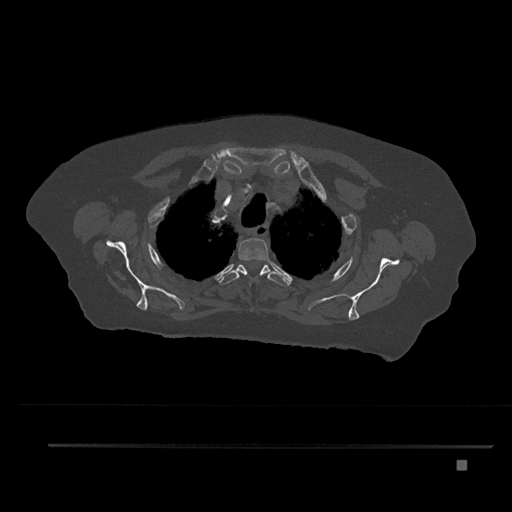
CT including the spine, one axial slice; slice 650 of 797 in the series (ordered by position); reconstruction kernel Br40s/3; bone window (W 1800 / L 400 HU); 0.5 mm slice thickness; 512 × 512 image matrix. Female patient, age 76 years. From the clinical record (not read from this slice): primary cancer: lung.
Outlined on this slice (semi-automatic segmentation, software-assisted and operator-edited):
- T2 vertebra: bounding box <238,238,271,273> (left, top, right, bottom; pixels)
- T3 vertebra: <218,261,289,287>